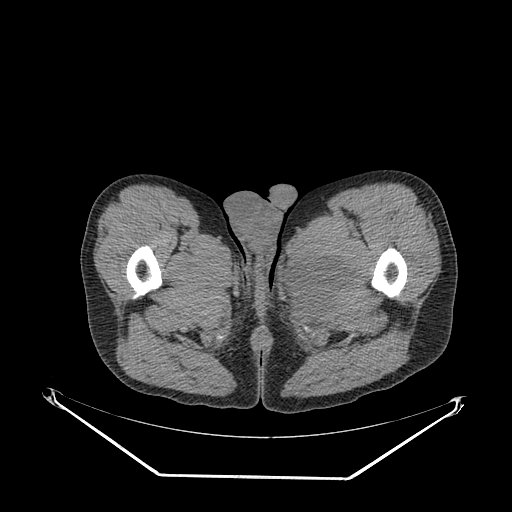
CT of an extremity soft-tissue mass (from a PET/CT study), one axial slice; slice 41 of 267 in the series (ordered by position); reconstruction kernel SOFT; soft-tissue window (W 400 / L 40 HU); 3.75 mm slice thickness; 512 × 512 image matrix, field of view 500 × 500 mm. Male patient. From the clinical record (not read from this slice): histological type: pleiomorphic liposarcoma; grade: high; site of the primary tumour: left thigh.
Annotated regions visible in this slice (expert contour drawn on MRI and transferred to this co-registered scan by the dataset authors):
- gross tumour volume including surrounding oedema: bounding box <288,253,353,321> (left, top, right, bottom; pixels)
- gross tumour volume (mass): <290,258,344,305>